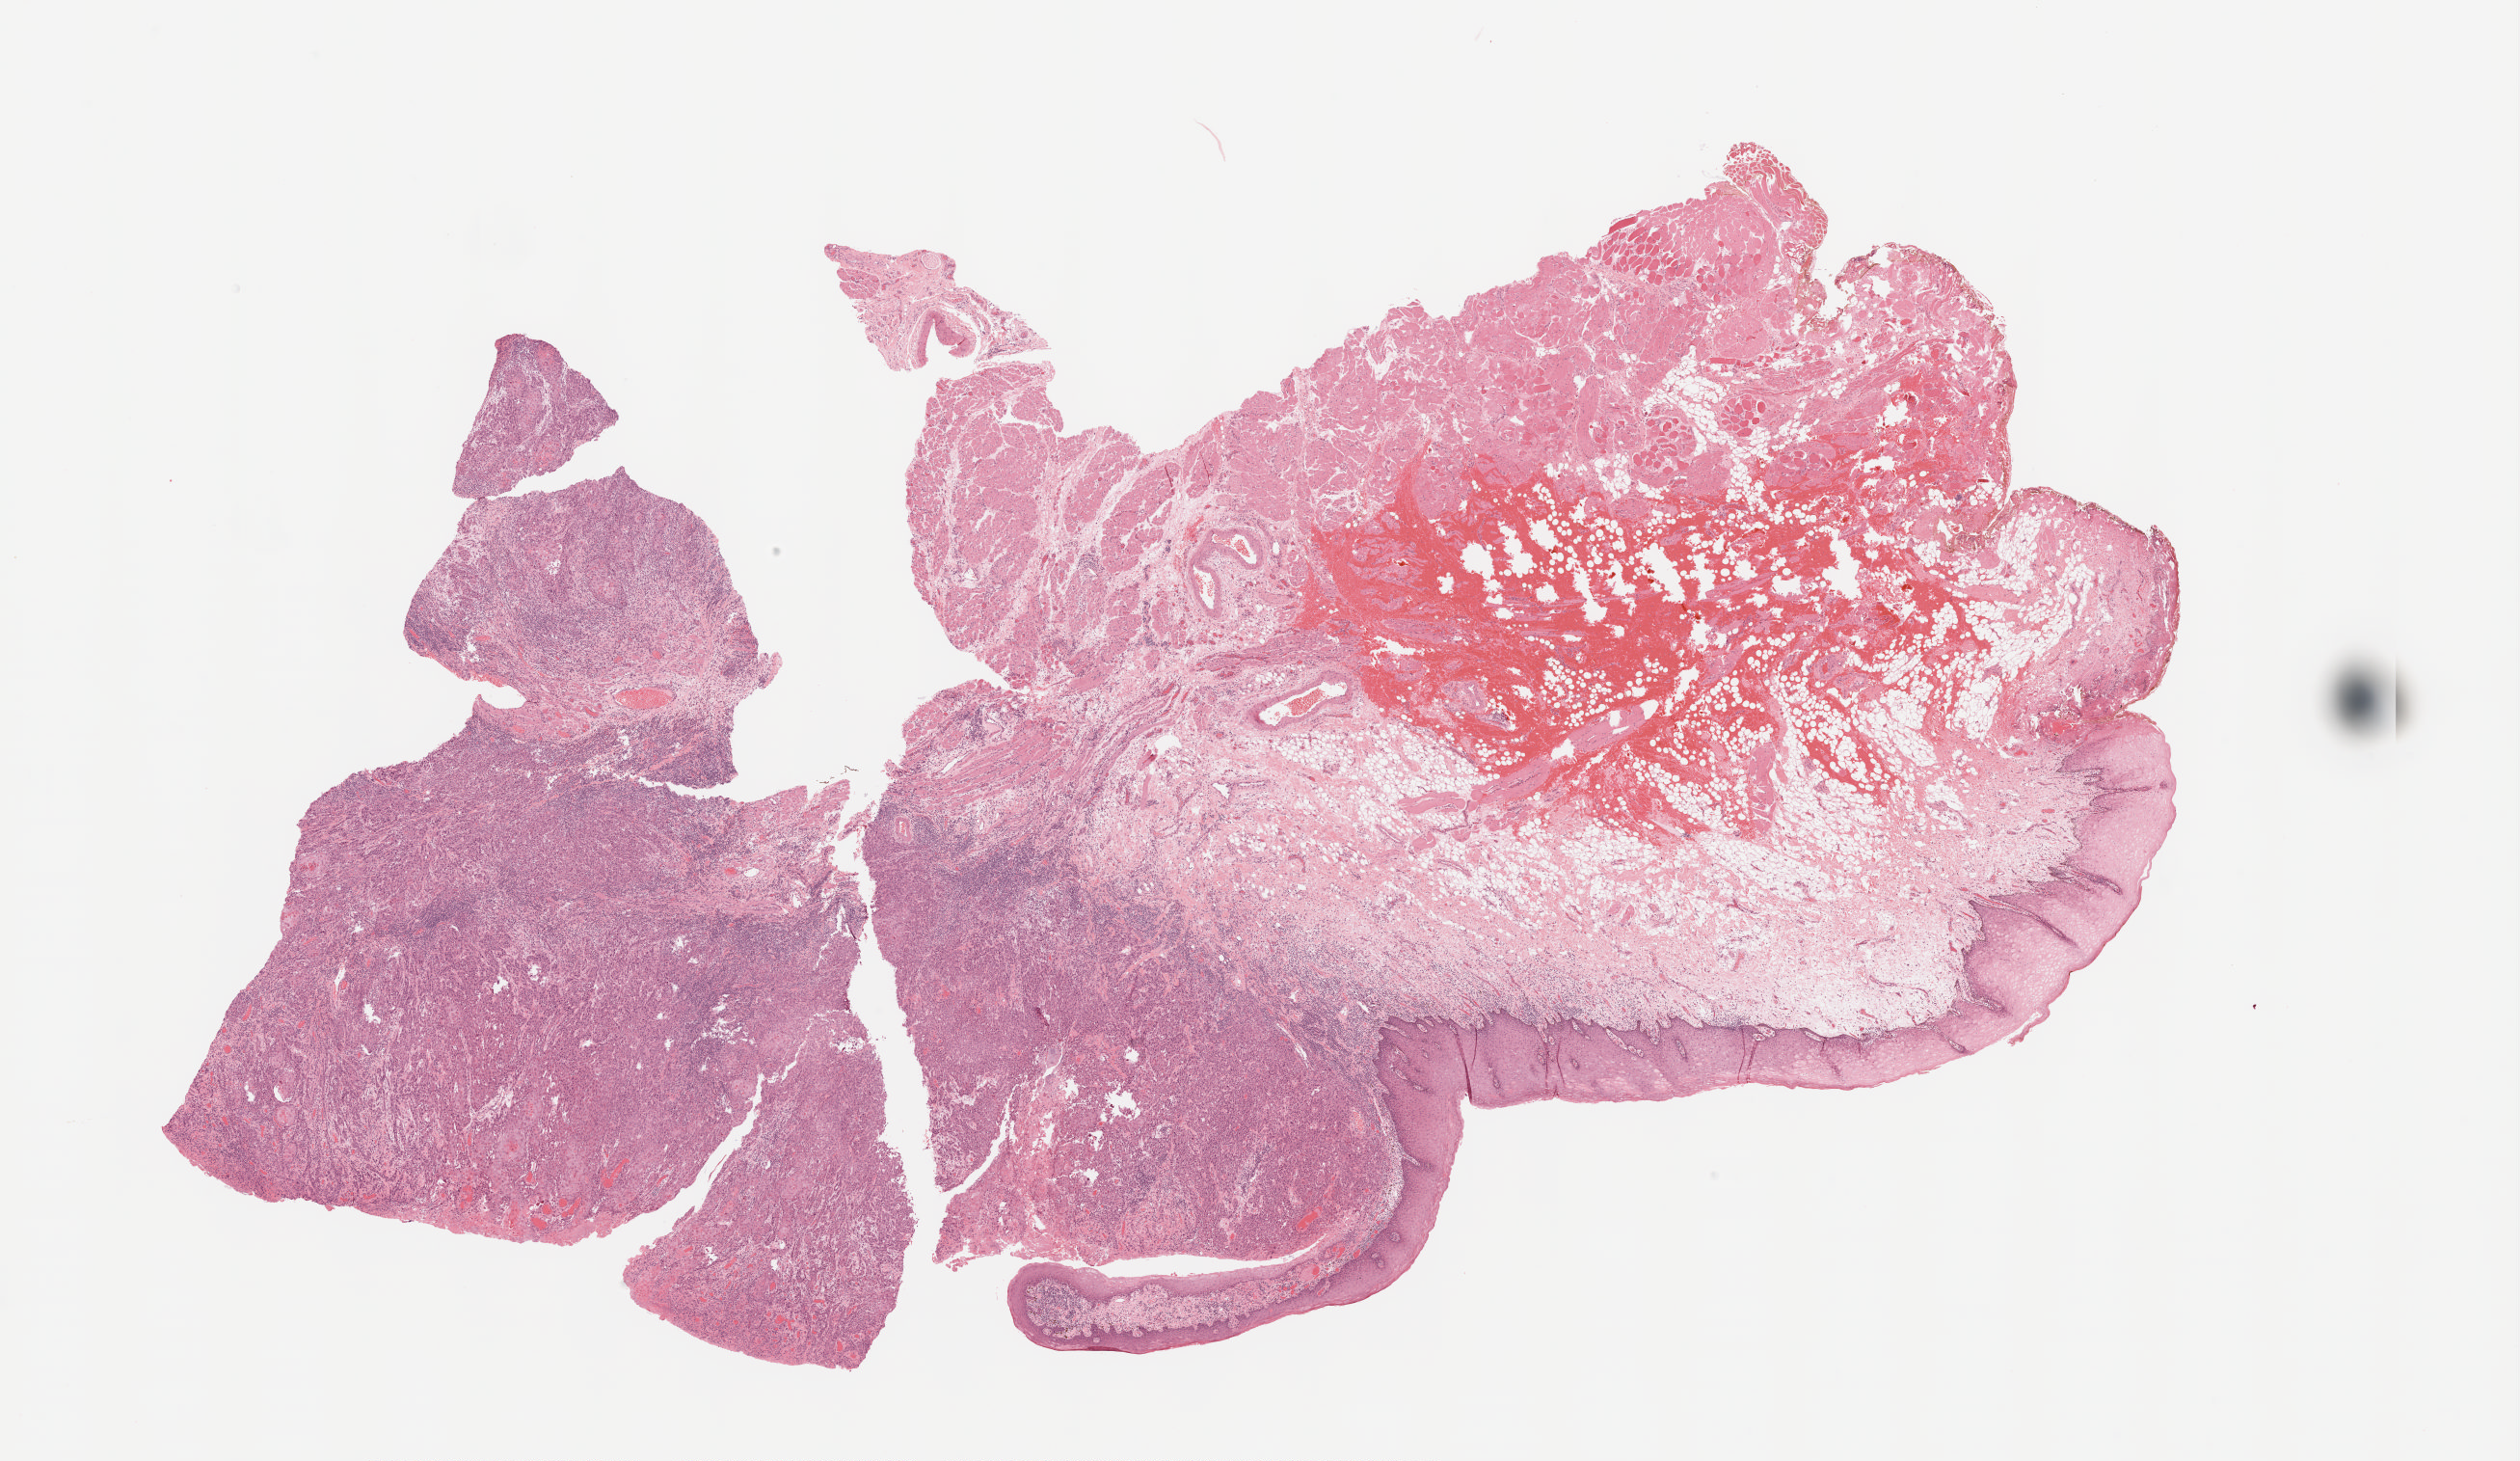
Whole-slide histology image, H&E — a low-resolution overview of the entire scanned area, about 21.0 x 12.2 mm; formalin-fixed paraffin-embedded (FFPE) diagnostic section; primary tumour sample from the head and neck. Male patient; age at initial diagnosis 63 years. Histologic grade: G2 (moderately differentiated).
Lymph nodes positive (case pathology): 0 of 23 examined. Laterality: right. Pathologic diagnosis: Squamous cell carcinoma, NOS (cheek mucosa). TNM: T2 N0 M0. AJCC pathologic stage: II (7th edition).